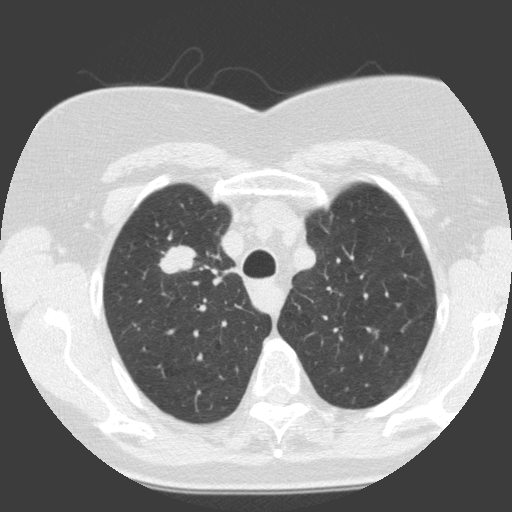
Low-dose screening chest CT, axial slice; first (baseline) screen; lung window (W 1500 / L -600 HU); 2 mm slice thickness; standard (soft-tissue) reconstruction kernel (C); 512 × 512 image matrix. Female participant, aged 68 years at enrolment. Current smoker at enrolment.
Lesion marked by an expert reader, bounding box (x1, y1, x2, y2) in pixels: (154, 240, 201, 284). Reader record for this screening exam (exam-level; its link to the box is not recorded): non-calcified nodule or mass ≥4 mm, right upper lobe, 19 × 12 mm, smooth margins, soft tissue attenuation.